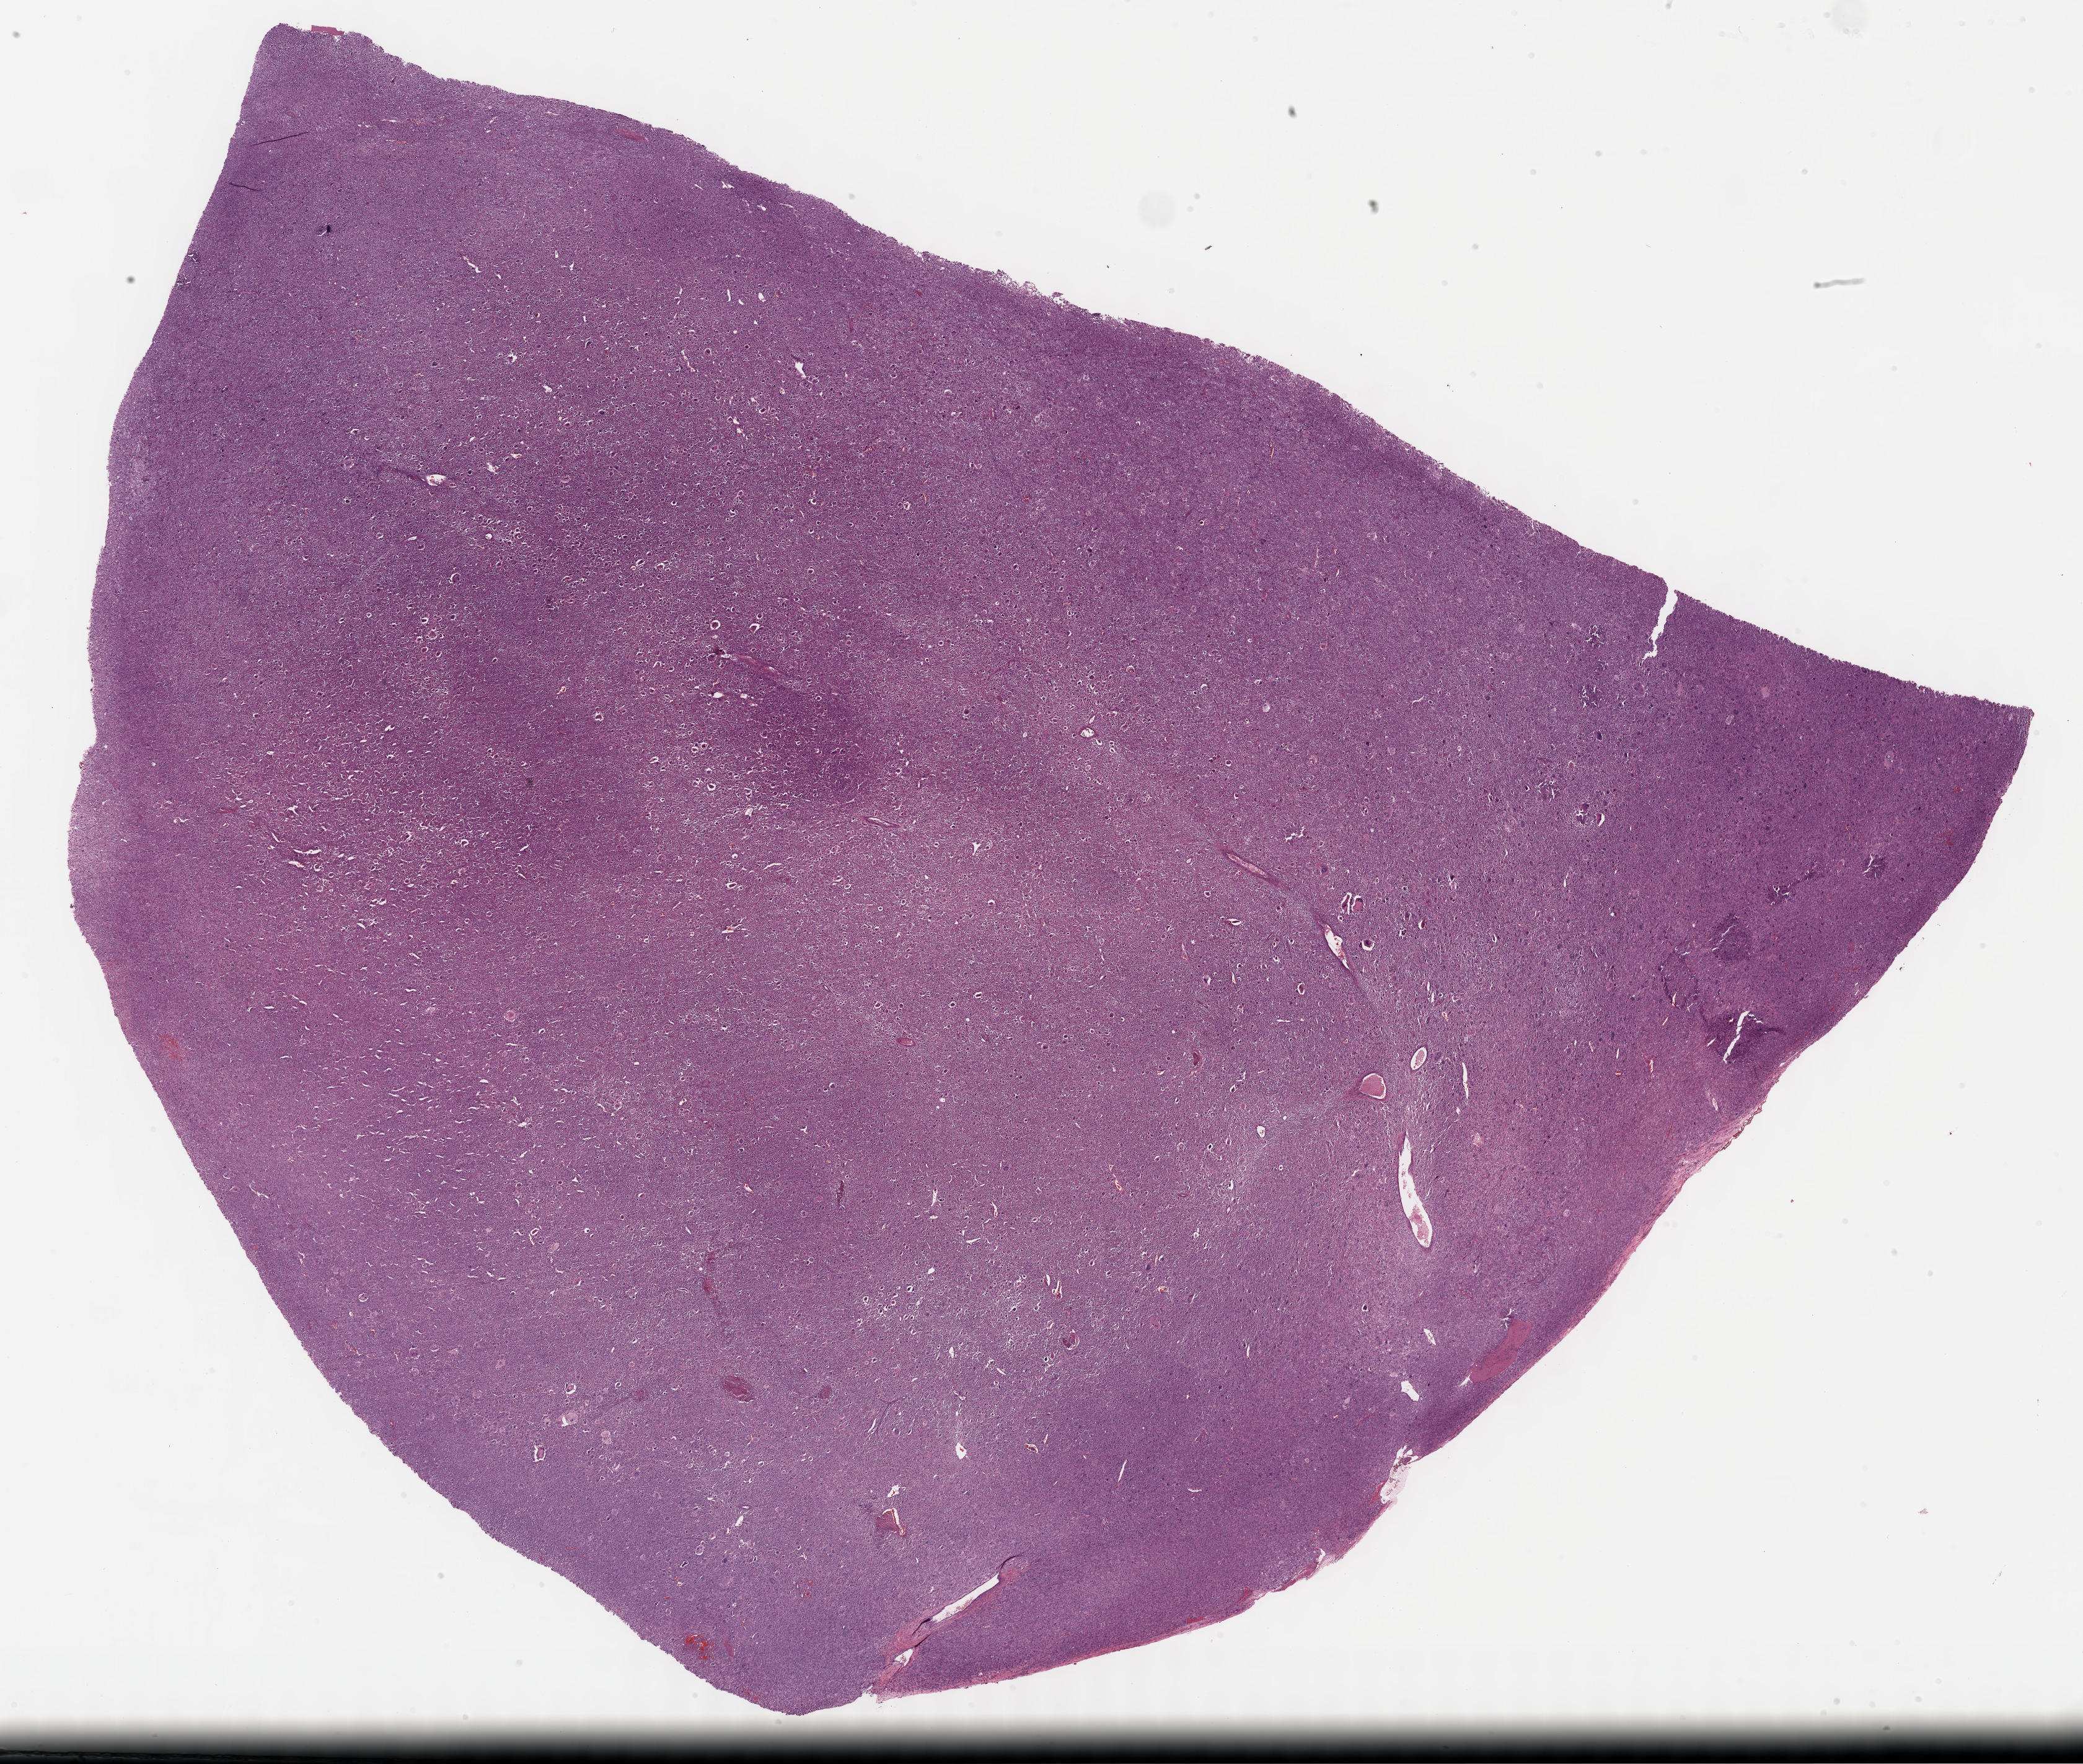
Hematoxylin and eosin (H&E) stained whole-slide image — shown as a low-resolution overview of the whole scanned area (about 27.2 x 23.0 mm, from a 40x scan). Formalin-fixed paraffin-embedded (FFPE) diagnostic section. Connective, subcutaneous and other soft tissues, primary tumour sample. Female patient; age at initial diagnosis 68 years.
Diagnosis: Undifferentiated sarcoma (connective, subcutaneous and other soft tissues of lower limb and hip).